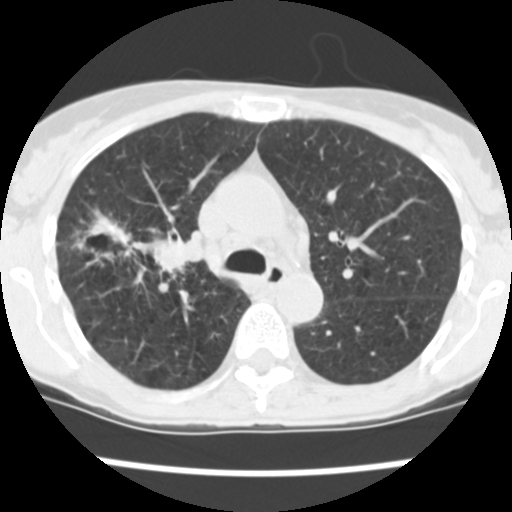
Axial slice from a low-dose chest CT screening exam, baseline screening round, lung window (W 1500 / L -600 HU), 2.5 mm slice thickness, 120 kVp, 512 × 512 image matrix, field of view 276 × 276 mm. Female, age 60 years at enrolment. Current smoker at enrolment.
• Expert-annotated lung lesion, bounding box <82,216,191,283> (left, top, right, bottom; pixels).
• The screening reader recorded 3 non-calcified nodules or masses ≥4 mm on this exam (right upper lobe, right upper lobe, right lower lobe); which of them this box marks is not recorded.
• Later outcome: lung cancer diagnosed 19 days after this screen — non-small cell carcinoma, right upper lobe, stage IV (AJCC 6th edition), 26 mm at pathology.